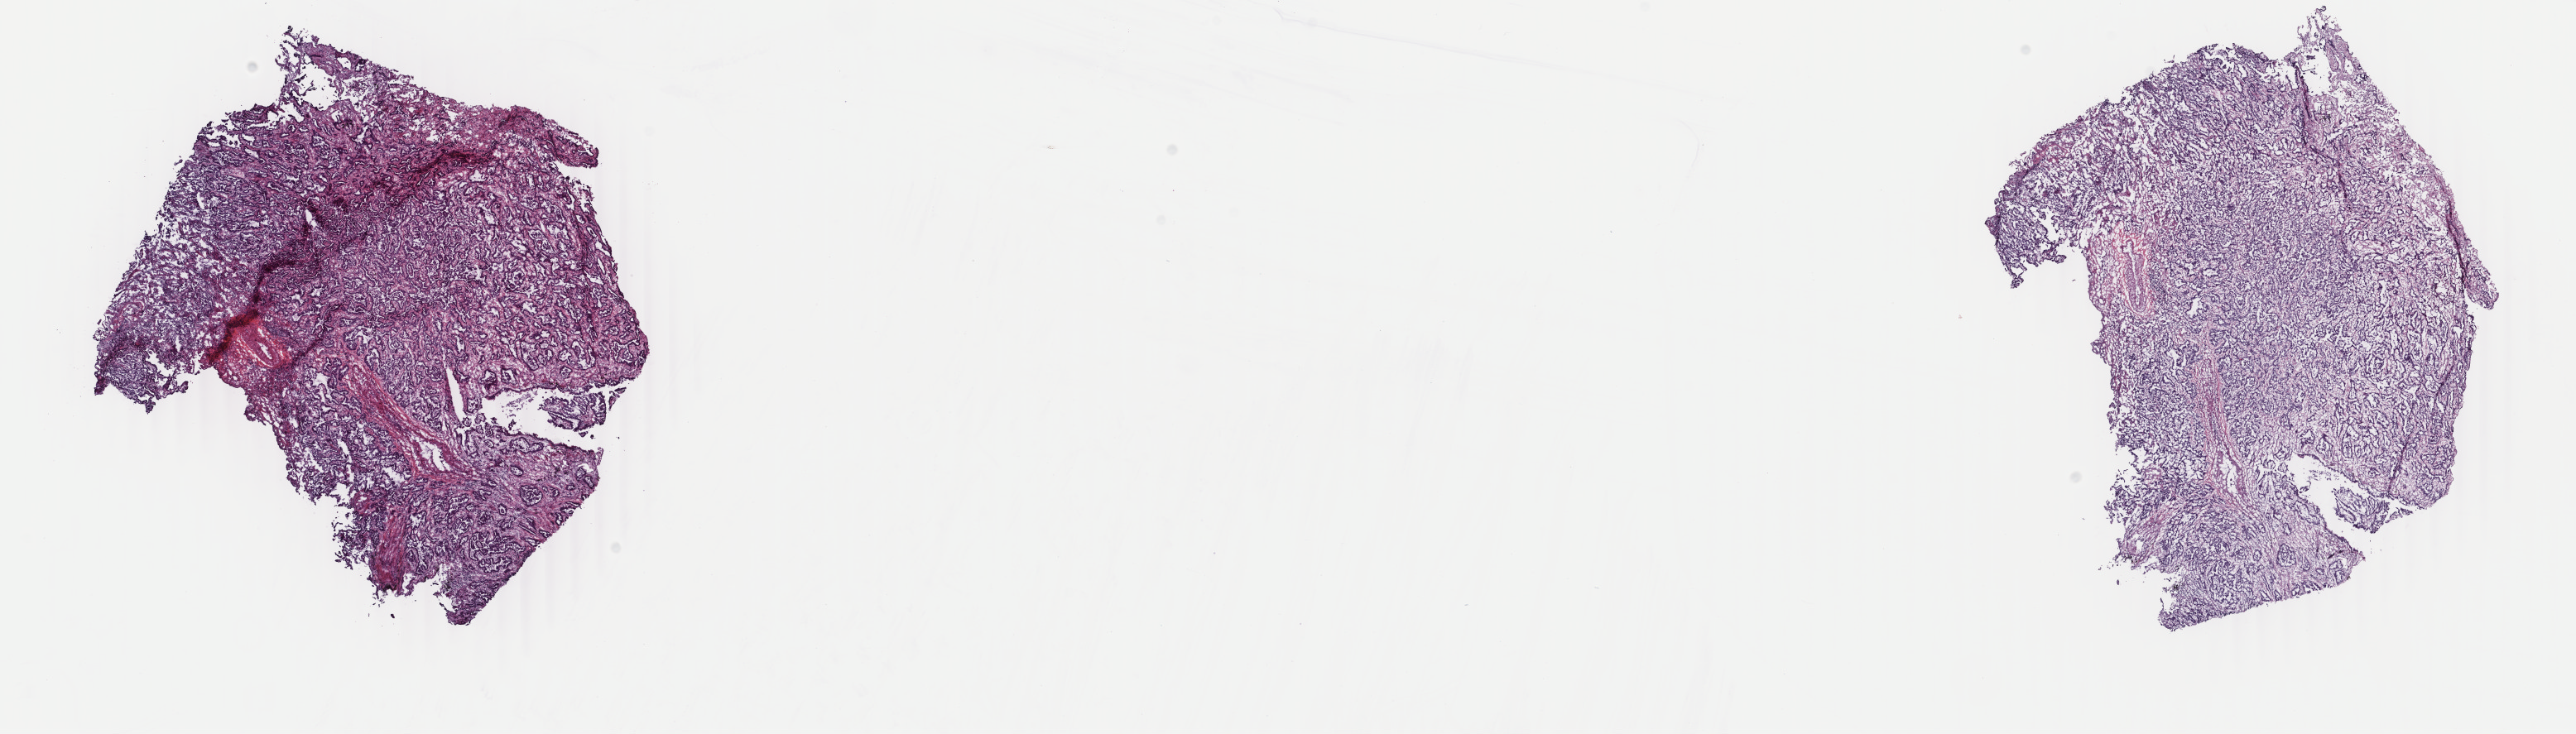
H&E whole-slide image — whole scanned area (about 24.7 x 7.1 mm, slide scanned at 40x) shown as a low-resolution overview; frozen section from the top of the tissue portion; lung, primary tumour sample. Patient: female, age at initial diagnosis 69 years. Slide review estimates, as recorded: tumour cells 100%, tumour nuclei 75%, normal cells 0%, stromal cells 0%, necrosis 0%. Inflammatory infiltration, as recorded: lymphocyte infiltration 2%, monocyte infiltration 2%, neutrophil infiltration 1%.
Laterality: right. AJCC pathologic stage: IA (7th edition). Pathologic diagnosis: Adenocarcinoma with mixed subtypes (upper lobe, lung).